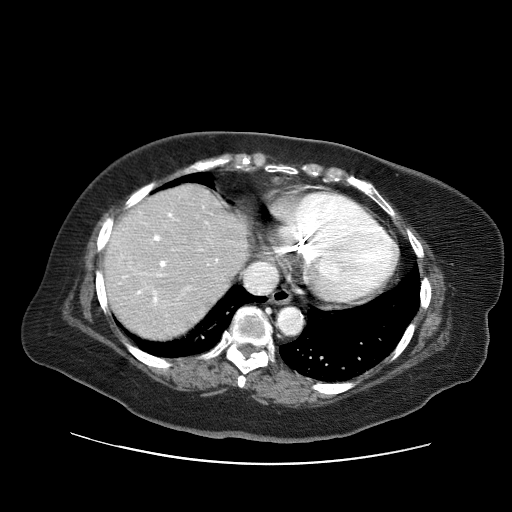
Contrast-enhanced abdominal CT (liver protocol), one axial slice. Position 55 of 71 along the scan axis. 120 kVp. Soft-tissue window (W 400 / L 40 HU). 2.5 mm slice thickness. 512 × 512 image matrix. From the clinical record (not read from this slice): diagnosis: hepatocellular carcinoma (patient treated with transarterial chemoembolisation; whether this scan precedes or follows treatment is not stated here); TNM stage (as recorded): Stage-II; Child-Pugh class: A; tumour differentiation: poorly differentiated; tumour size: 5 cm.
Annotated regions visible in this slice (semi-automatic segmentation, software-assisted and operator-edited):
- liver parenchyma outside the tumour (the mass and vessels are separate outlines, so this box may not span the whole liver): bounding box (x1, y1, x2, y2) in pixels: (104, 184, 248, 338)
- liver vessels: (119, 206, 218, 305)